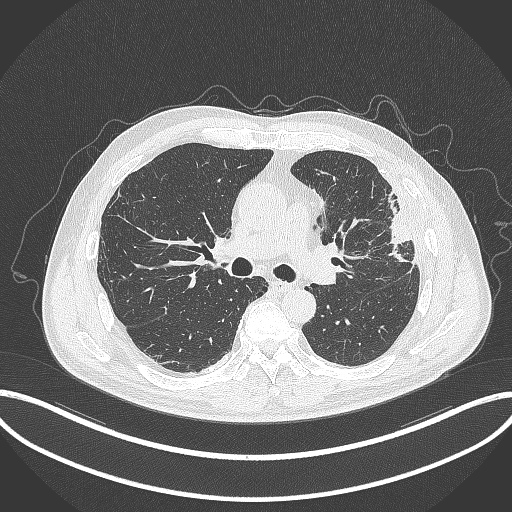
Chest CT, one axial slice. Slice 204 of 382 in the series (ordered by position). 120 kVp. Lung window (W 1500 / L -600 HU). 1 mm slice thickness. 512 × 512 image matrix, field of view 415 × 415 mm. Male patient, age 64 years. From the clinical record (not read from this slice): clinical TNM (as recorded): T4 N1 M0; histopathological grade: G3.
Outlined on this slice (bounding box drawn by a radiologist):
- lung tumour (recorded histology: adenocarcinoma): box from (x=378, y=188) to (x=419, y=264) px